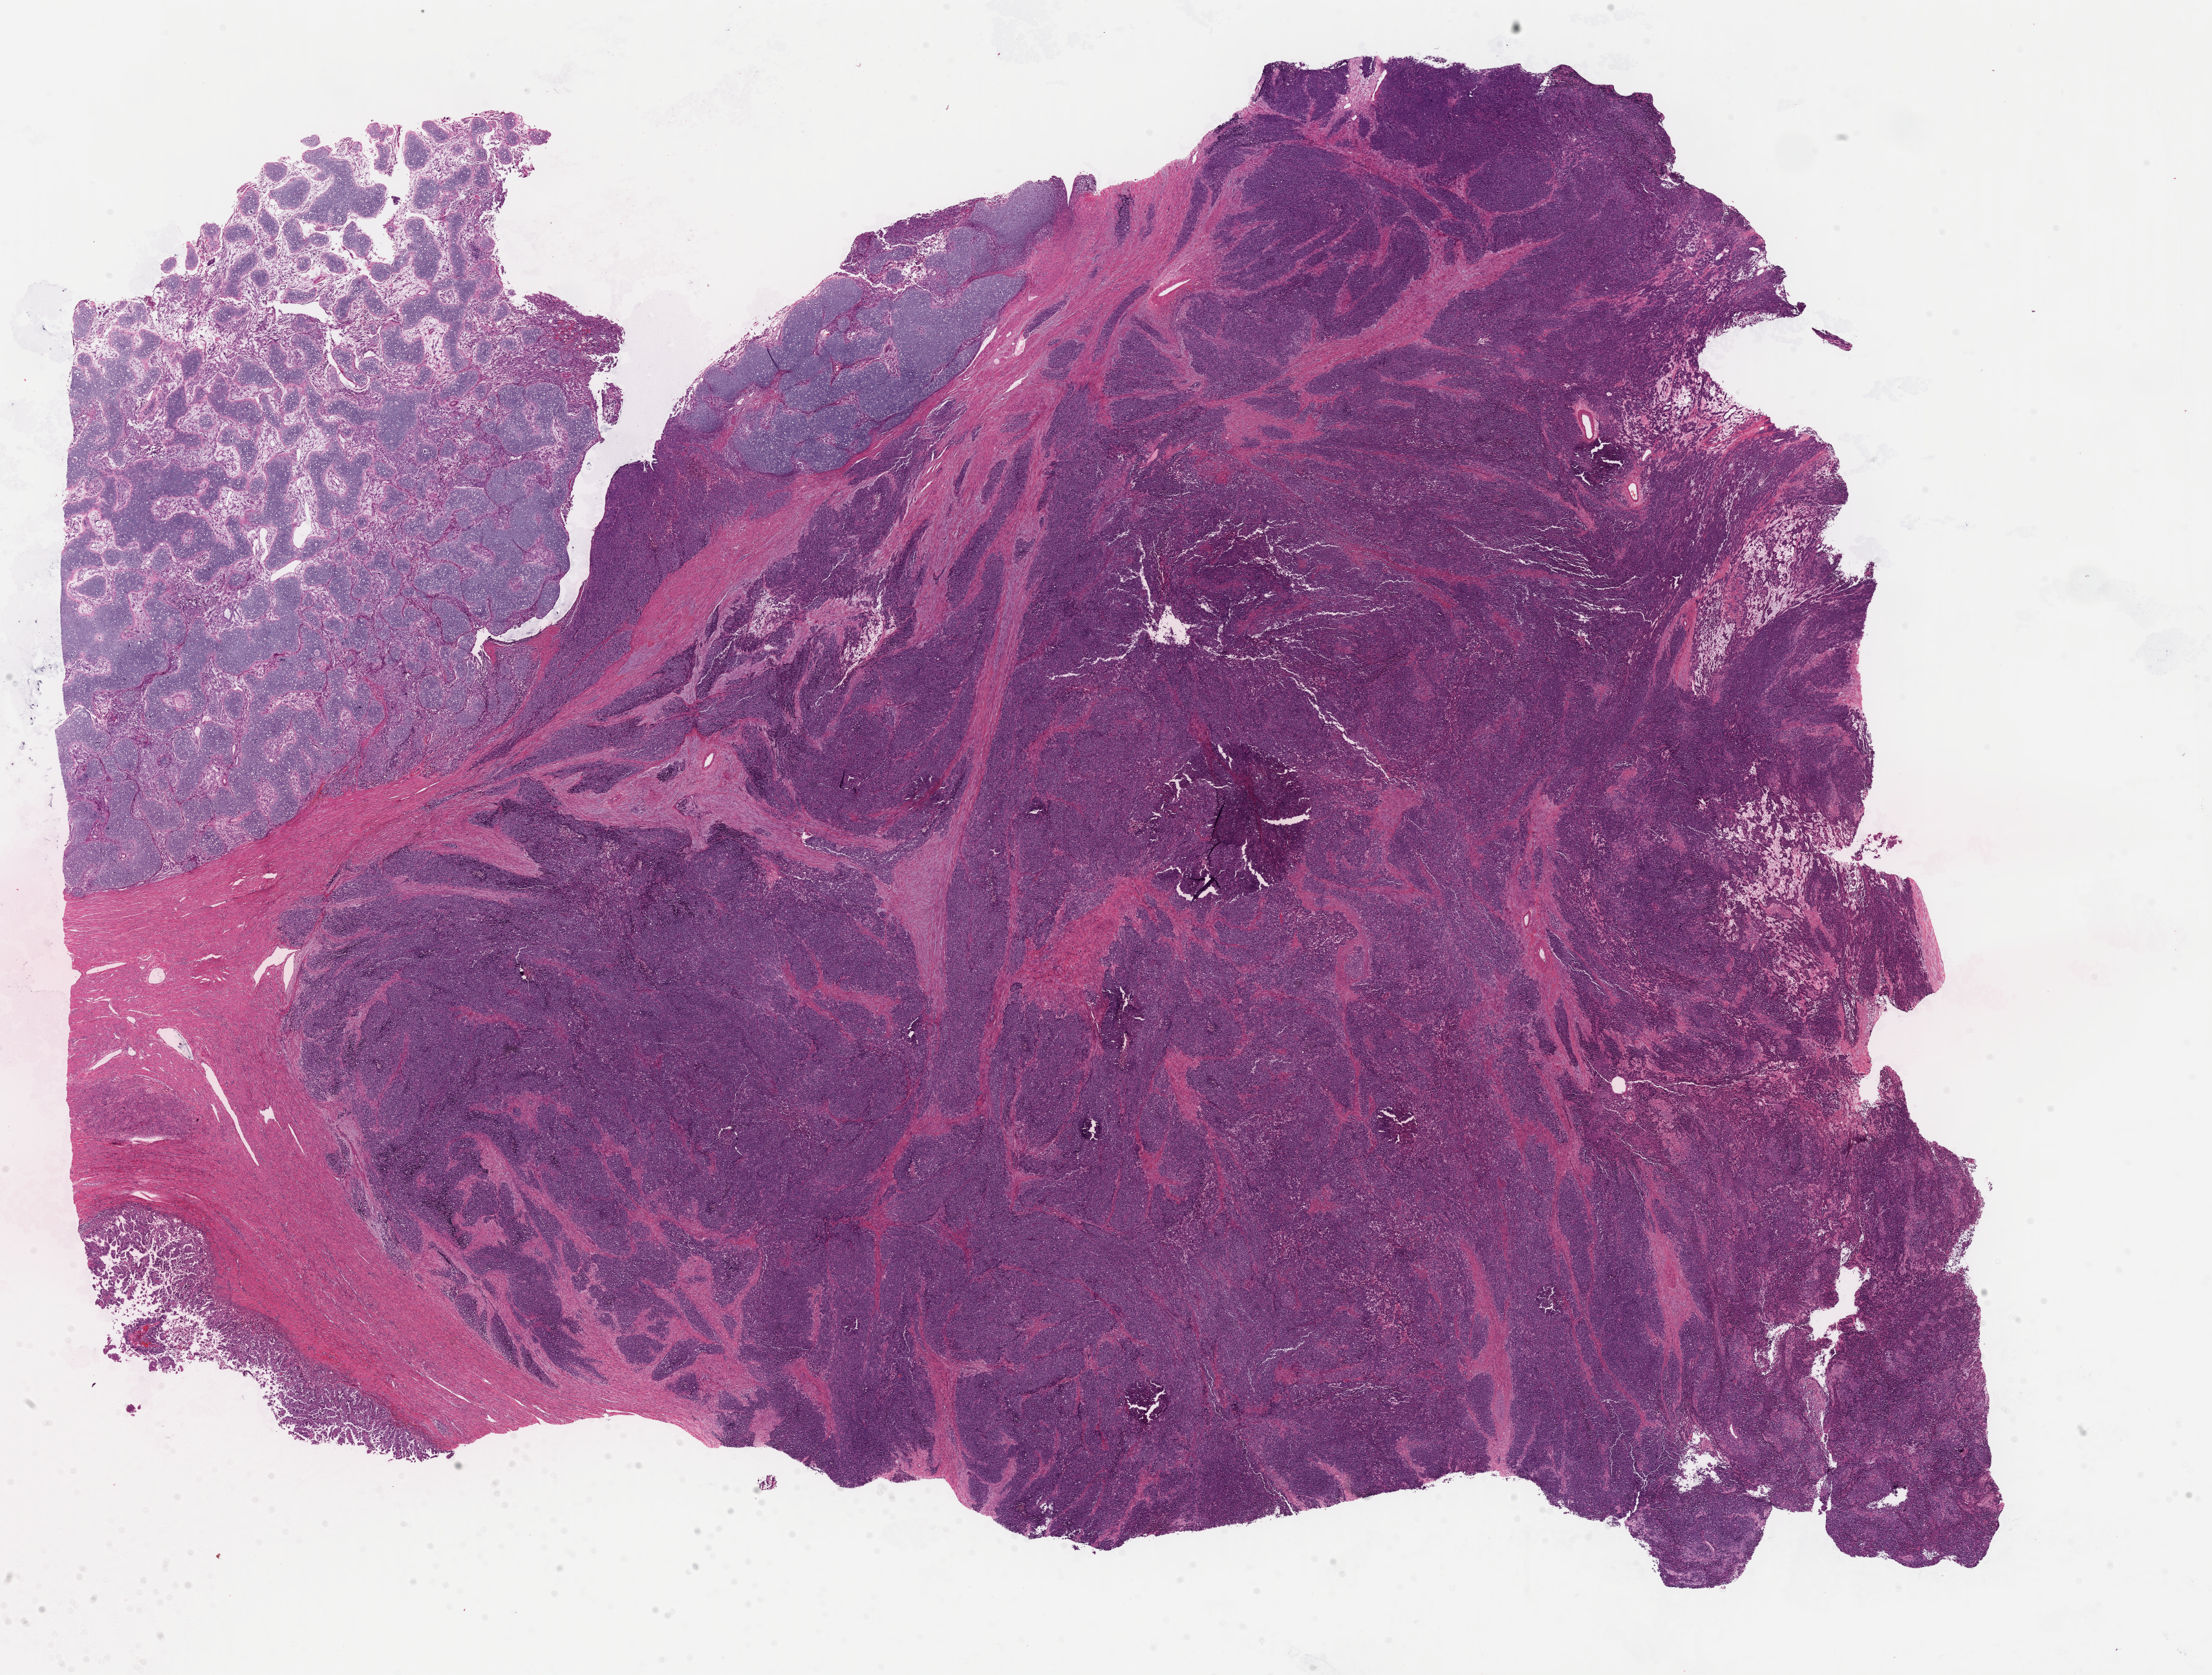
Hematoxylin and eosin (H&E) stained whole-slide image — whole scanned area (about 27.0 x 20.4 mm) shown as a low-resolution overview; formalin-fixed paraffin-embedded (FFPE) diagnostic section; uterus, primary tumour sample. Female patient.
* pathologic diagnosis: Mullerian mixed tumor (endometrium)
* FIGO stage: IC